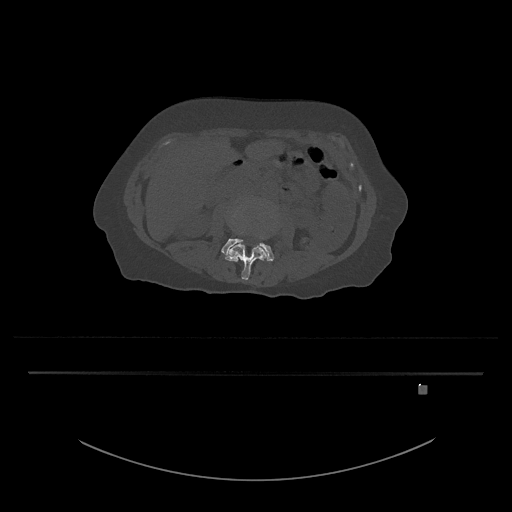
CT including the spine, one axial slice; position 399 of 797 along the scan axis; reconstruction kernel Br40s/3; 120 kVp; bone window (W 1800 / L 400 HU); 0.5 mm slice thickness; 512 × 512 image matrix. Female patient, age 57 years. Case-level facts recorded for this patient, not image findings: primary cancer: cervical.
Outlined on this slice (semi-automatically segmented with operator editing):
- L3 vertebra: bounding box [x1, y1, x2, y2] px = [224, 229, 267, 280]
- L4 vertebra: [221, 215, 274, 262]